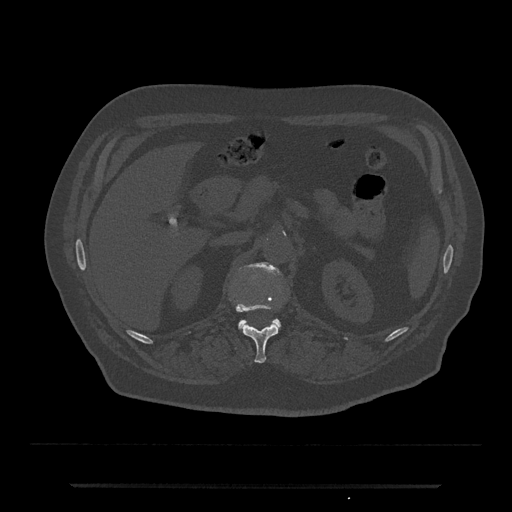
CT including the spine, one axial slice; position 574 of 797 along the scan axis; bone window (W 1800 / L 400 HU); 0.5 mm slice thickness; 512 × 512 image matrix, field of view 434 × 434 mm. Patient: male, 80 years. Case-level facts recorded for this patient, not image findings: primary cancer: prostate; vertebrae with lytic lesions (as recorded): L1, T11.
Annotated regions visible in this slice (semi-automatically segmented with operator editing):
- L1 vertebra: bounding box [x1, y1, x2, y2] px = [238, 262, 282, 329]
- T12 vertebra: [235, 301, 280, 363]